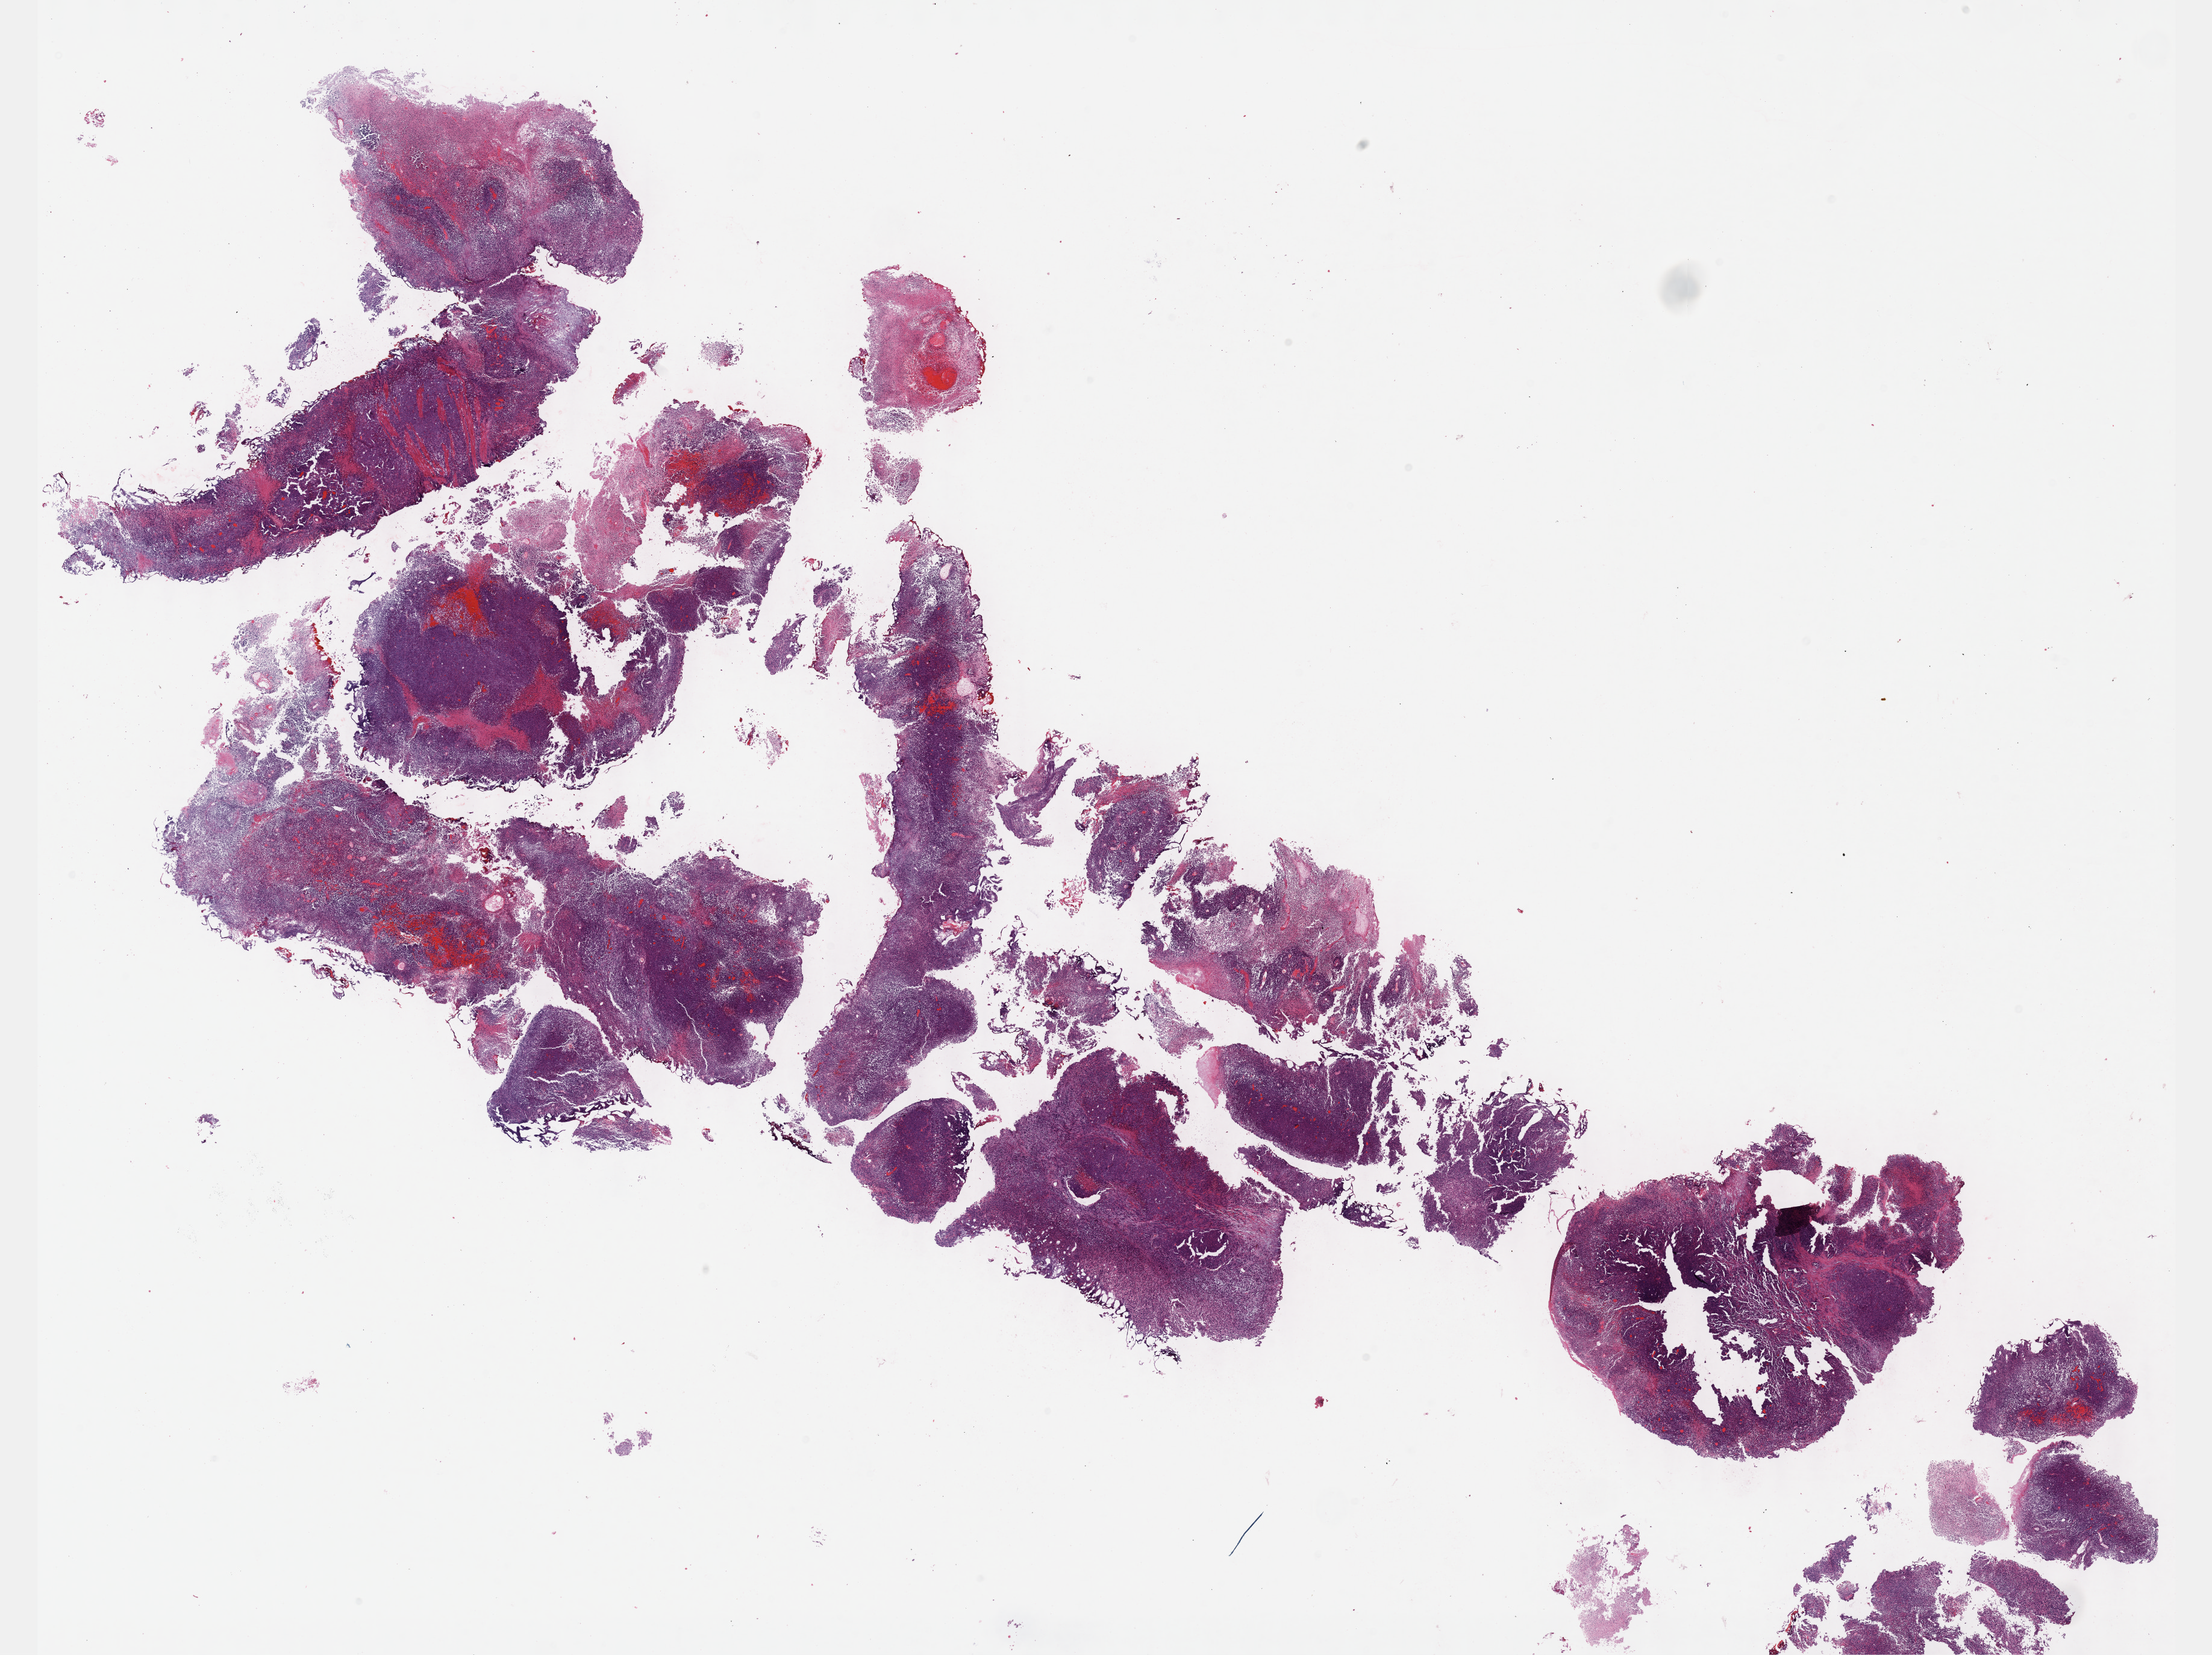
Digitized H&E tissue section (whole slide) — low-resolution overview of the scanned area, about 29.7 x 22.2 mm; formalin-fixed paraffin-embedded (FFPE) diagnostic section; bladder, primary tumour sample. Patient: male, age at initial diagnosis 49 years. Histologic grade: high grade.
Histologic diagnosis: Transitional cell carcinoma (lateral wall of bladder). AJCC pathologic stage: III (7th edition).